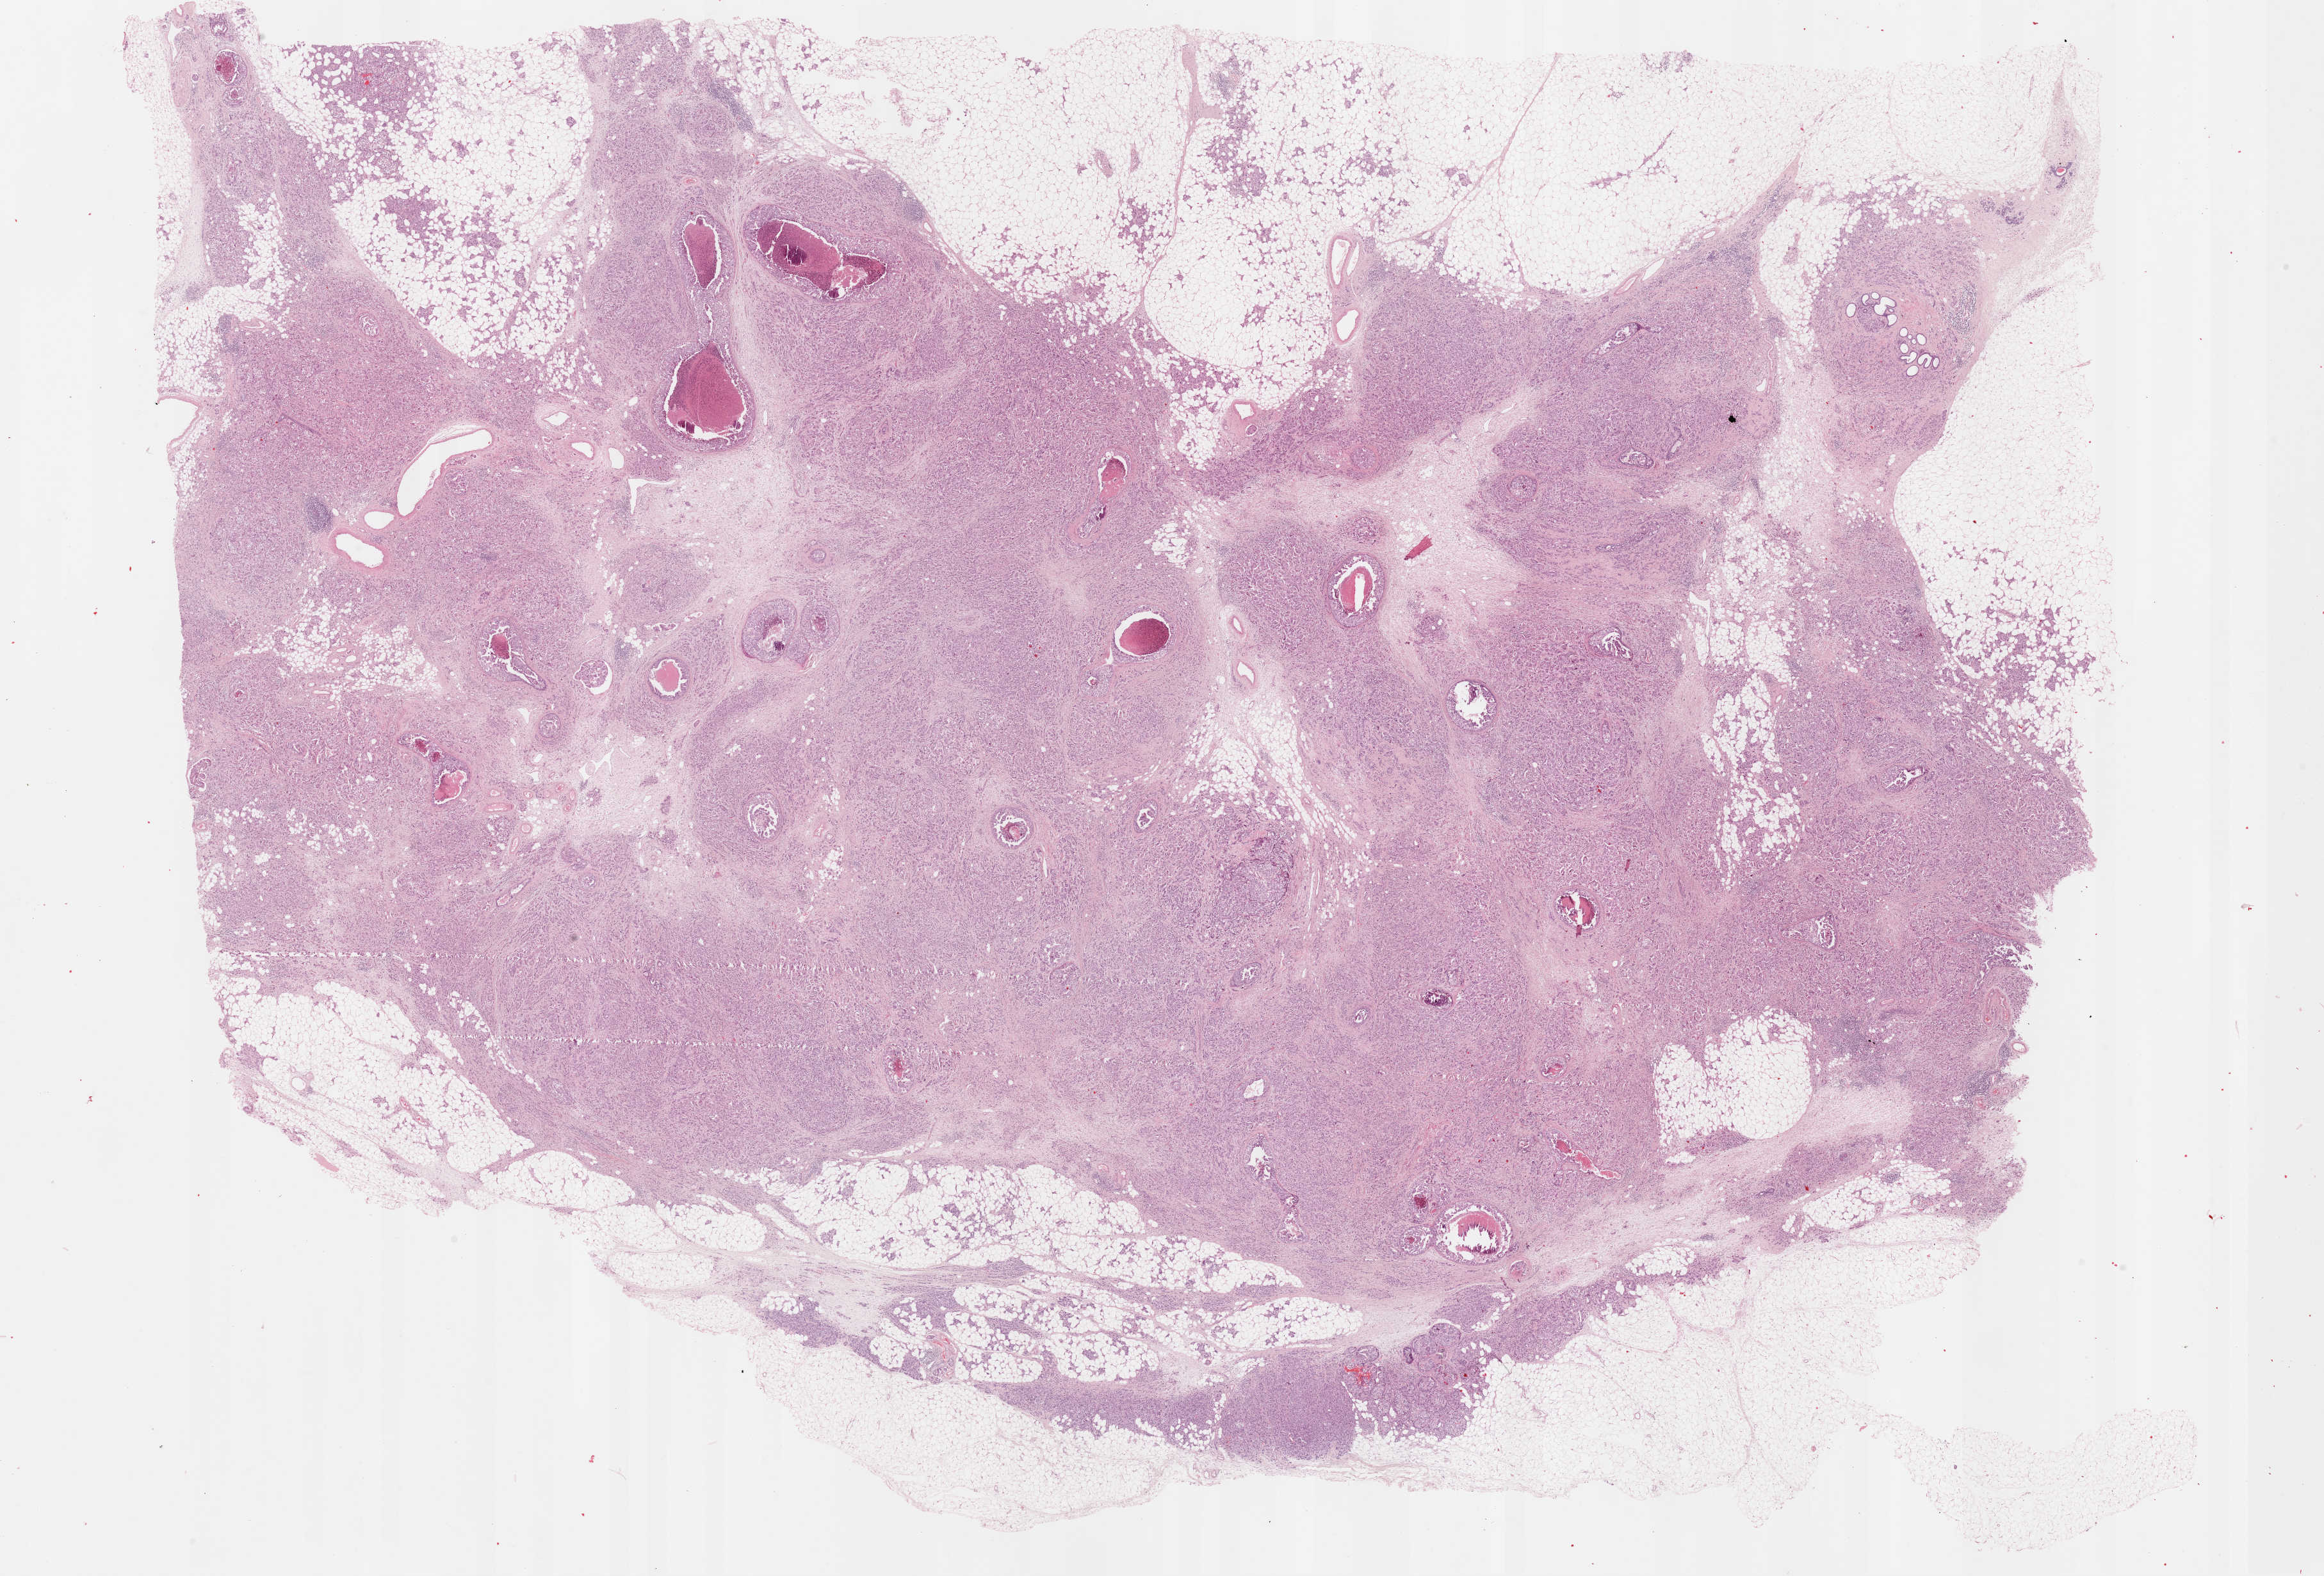
Whole-slide histology image, H&E — a low-resolution overview of the entire scanned area, about 28.7 x 19.4 mm (slide scanned at 40x); formalin-fixed paraffin-embedded (FFPE) diagnostic section; sample: primary tumour, breast. Patient: female, age at initial diagnosis 41 years.
Pathologic diagnosis: Infiltrating duct carcinoma, NOS.